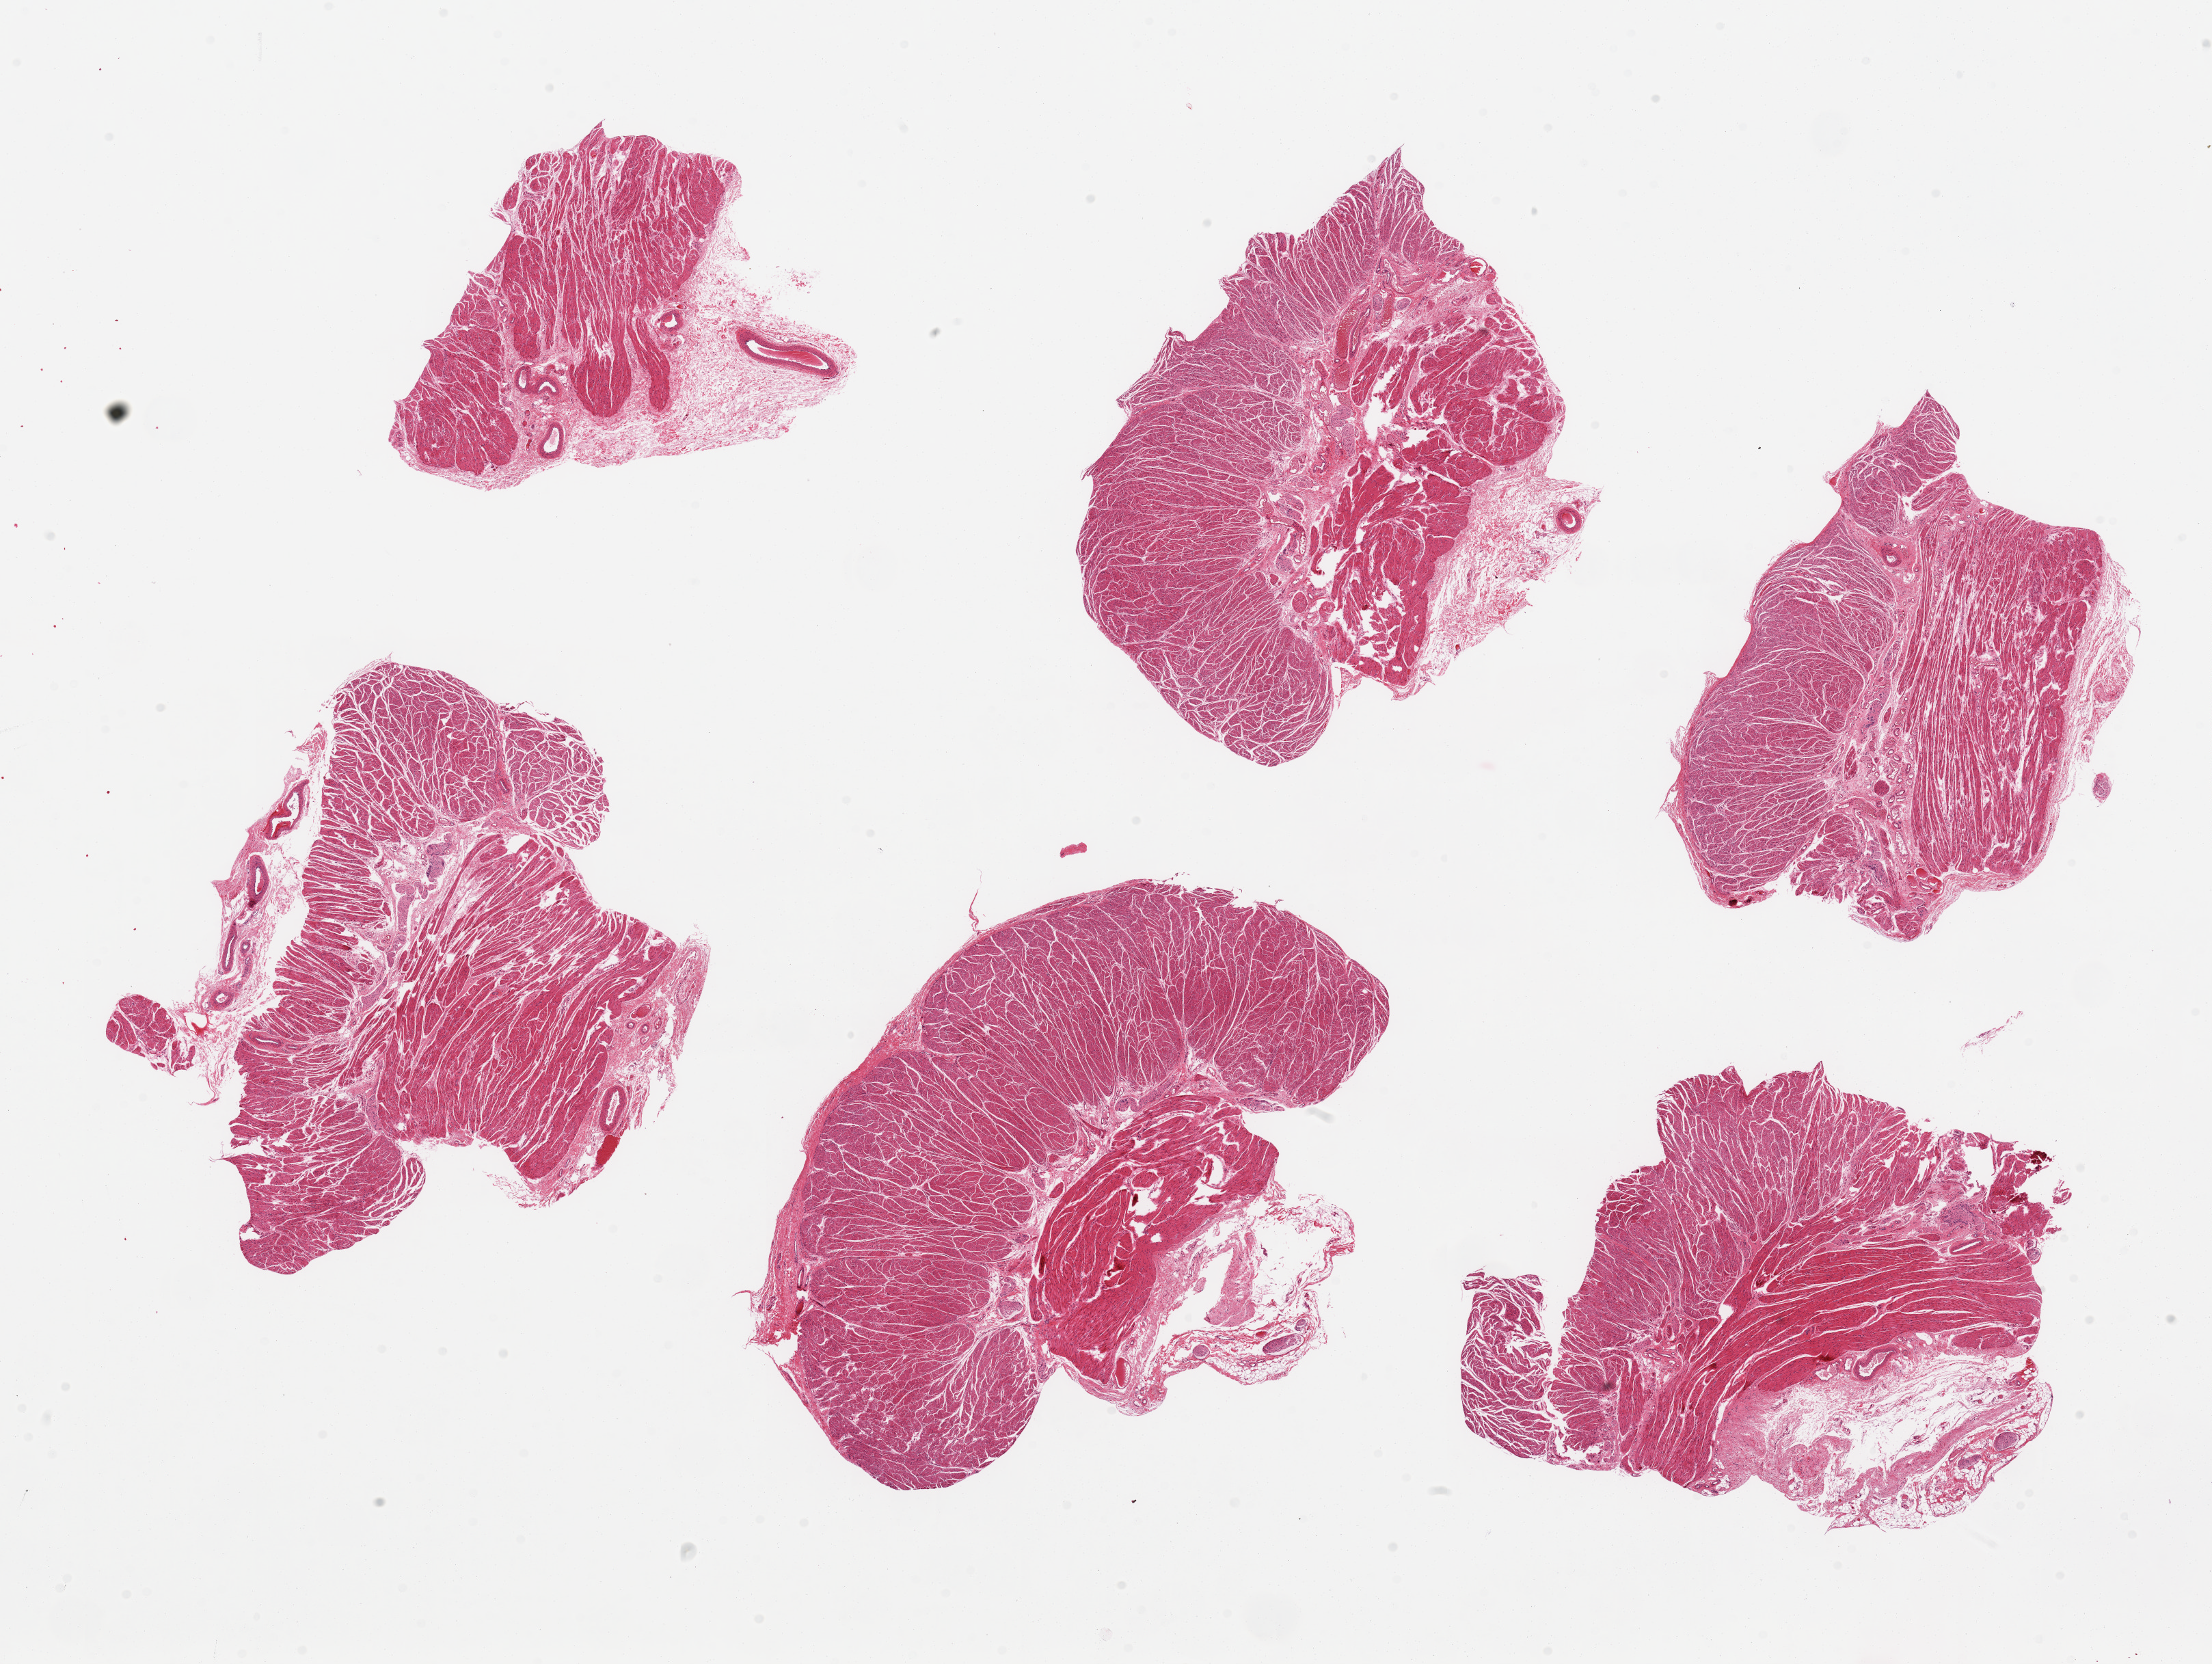
Digitized H&E-stained section, whole scanned area (about 25.6 x 19.3 mm, from a 20x scan) shown as a low-resolution overview. PAXgene-fixed, paraffin-embedded tissue. Section of gastroesophageal junction (target tissue). Donor tissue sample. Donor sex: female.
Review note (as recorded): 6 pieces, well trimmed.